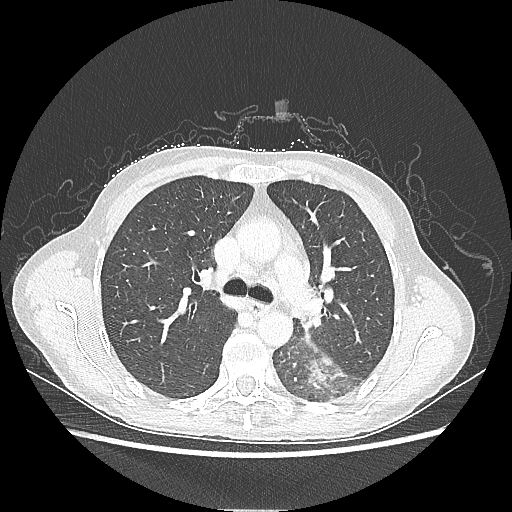
Chest CT, one axial slice; slice 142 of 220 in the series (ordered by position); 80 kVp; lung window (W 1500 / L -600 HU); 512 × 512 image matrix, field of view 360 × 360 mm. Female patient, age 53 years. From the clinical record (not read from this slice): clinical TNM (as recorded): T3 N0 M0.
Structures marked on this image (rectangle marked by the reading radiologist):
- lung tumour (recorded histology: adenocarcinoma): bounding box <303,358,343,389> (left, top, right, bottom; pixels)